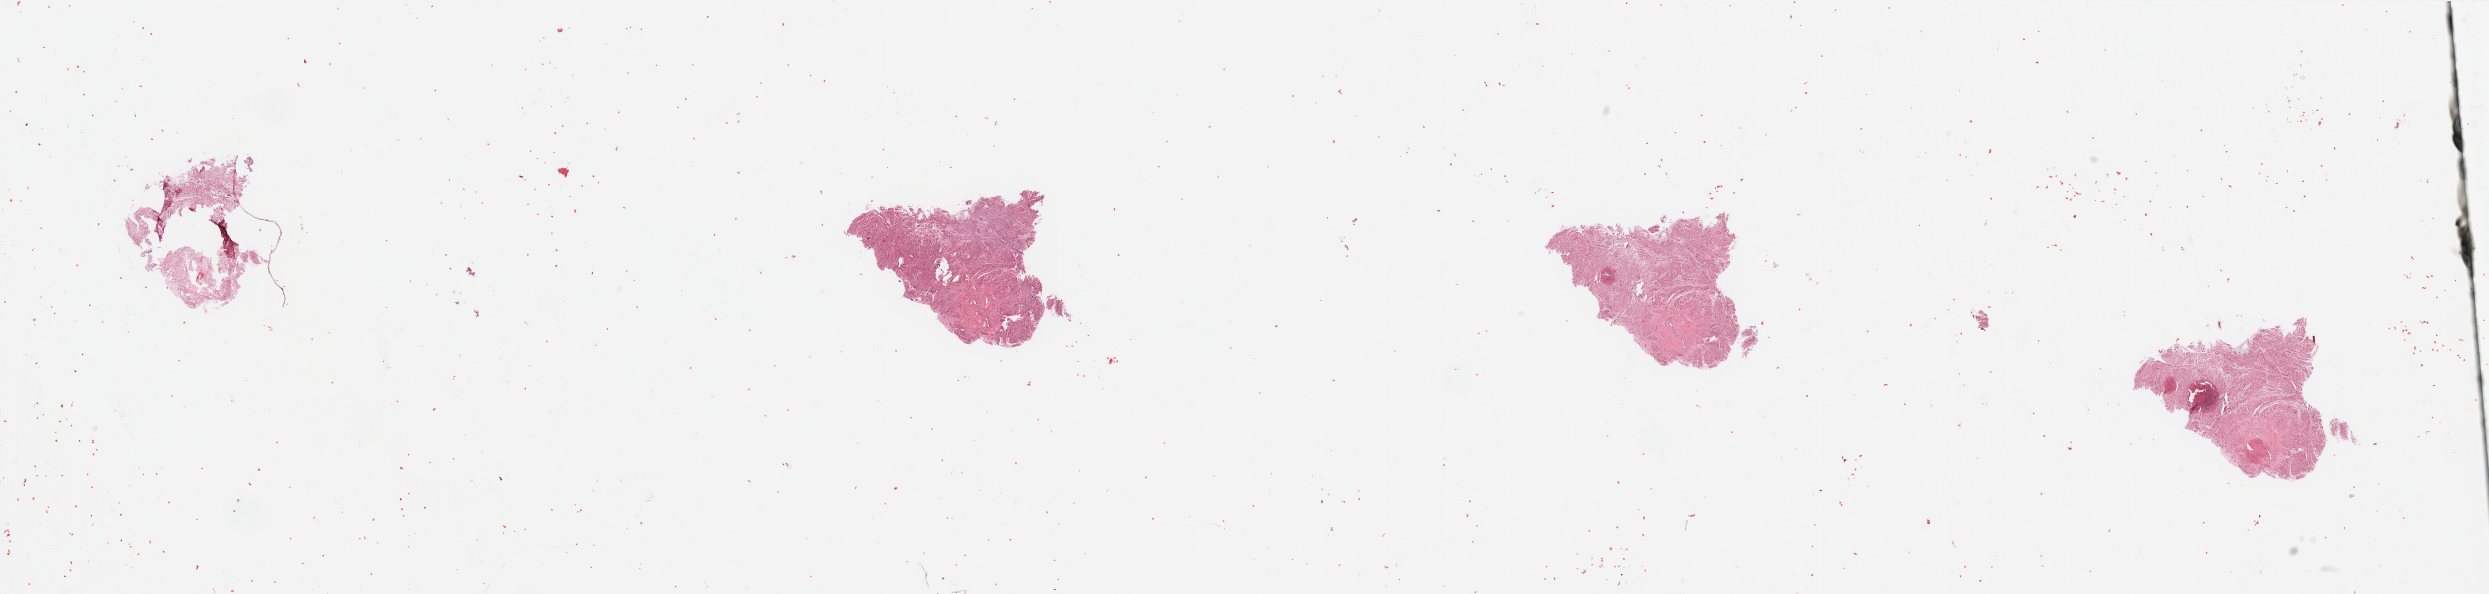
Digitized Hematoxylin and eosin (H&E) stained tissue section (whole slide), a low-resolution overview of the entire scanned area, about 39.4 x 9.4 mm (slide scanned at 20x). Uterus, normal (non-tumour) tissue. Female, 58 y/o.
• this section: normal (non-tumour) tissue from the same patient
• patient diagnosis: Endometrioid adenocarcinoma, NOS